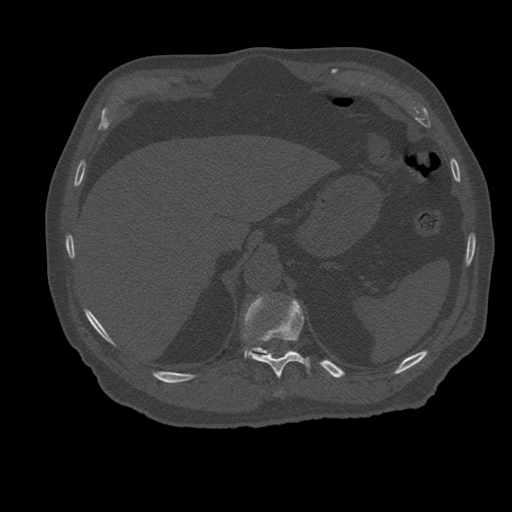
CT including the spine, one axial slice; slice 278 of 399 in the series (ordered by position); 120 kVp; bone window (W 1800 / L 400 HU); 512 × 512 image matrix, field of view 407 × 407 mm. Patient age 73 years. From the clinical record (not read from this slice): primary cancer: prostate.
Annotated regions visible in this slice (semi-automatic segmentation, software-assisted and operator-edited):
- T11 vertebra: bounding box (x1, y1, x2, y2) in pixels: (249, 300, 311, 378)
- T12 vertebra: (244, 296, 295, 358)